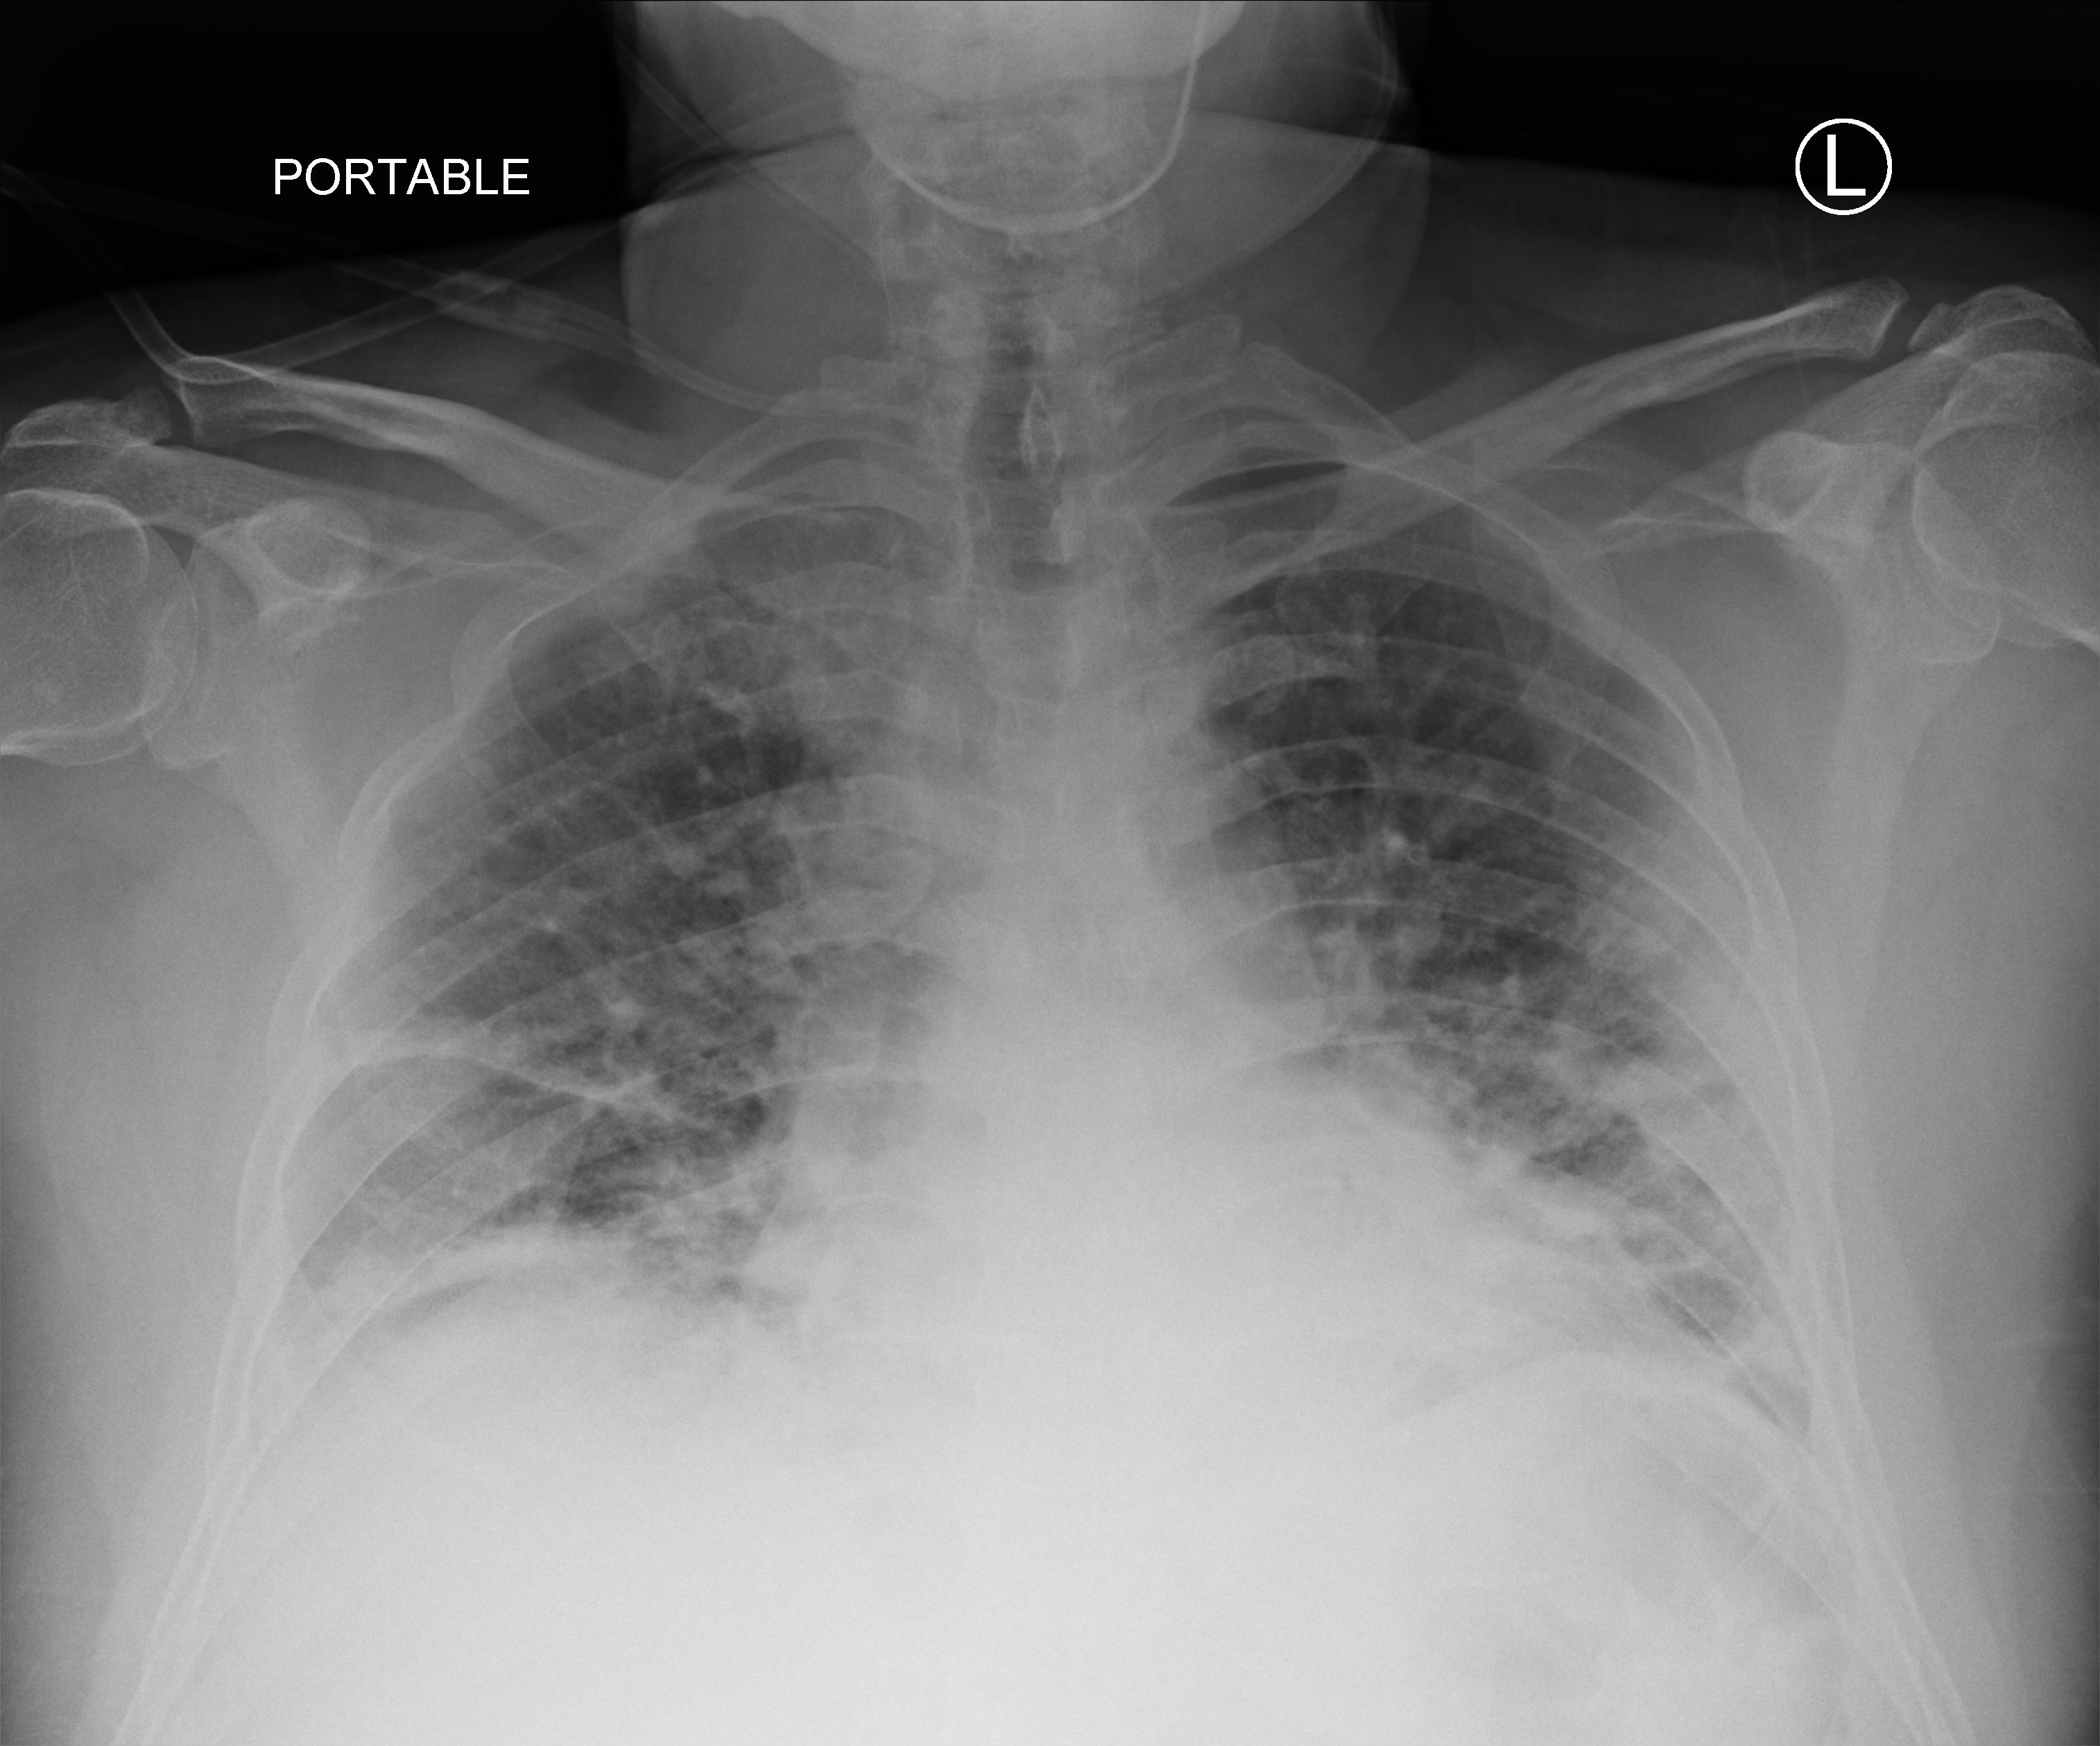
Portable chest radiograph, anteroposterior (AP) projection. Male patient hospitalised with COVID-19, age 18–59 years.
Admission-level facts for this patient (not findings on this image; timing relative to this image not recorded): chronic kidney disease (admission record): no.